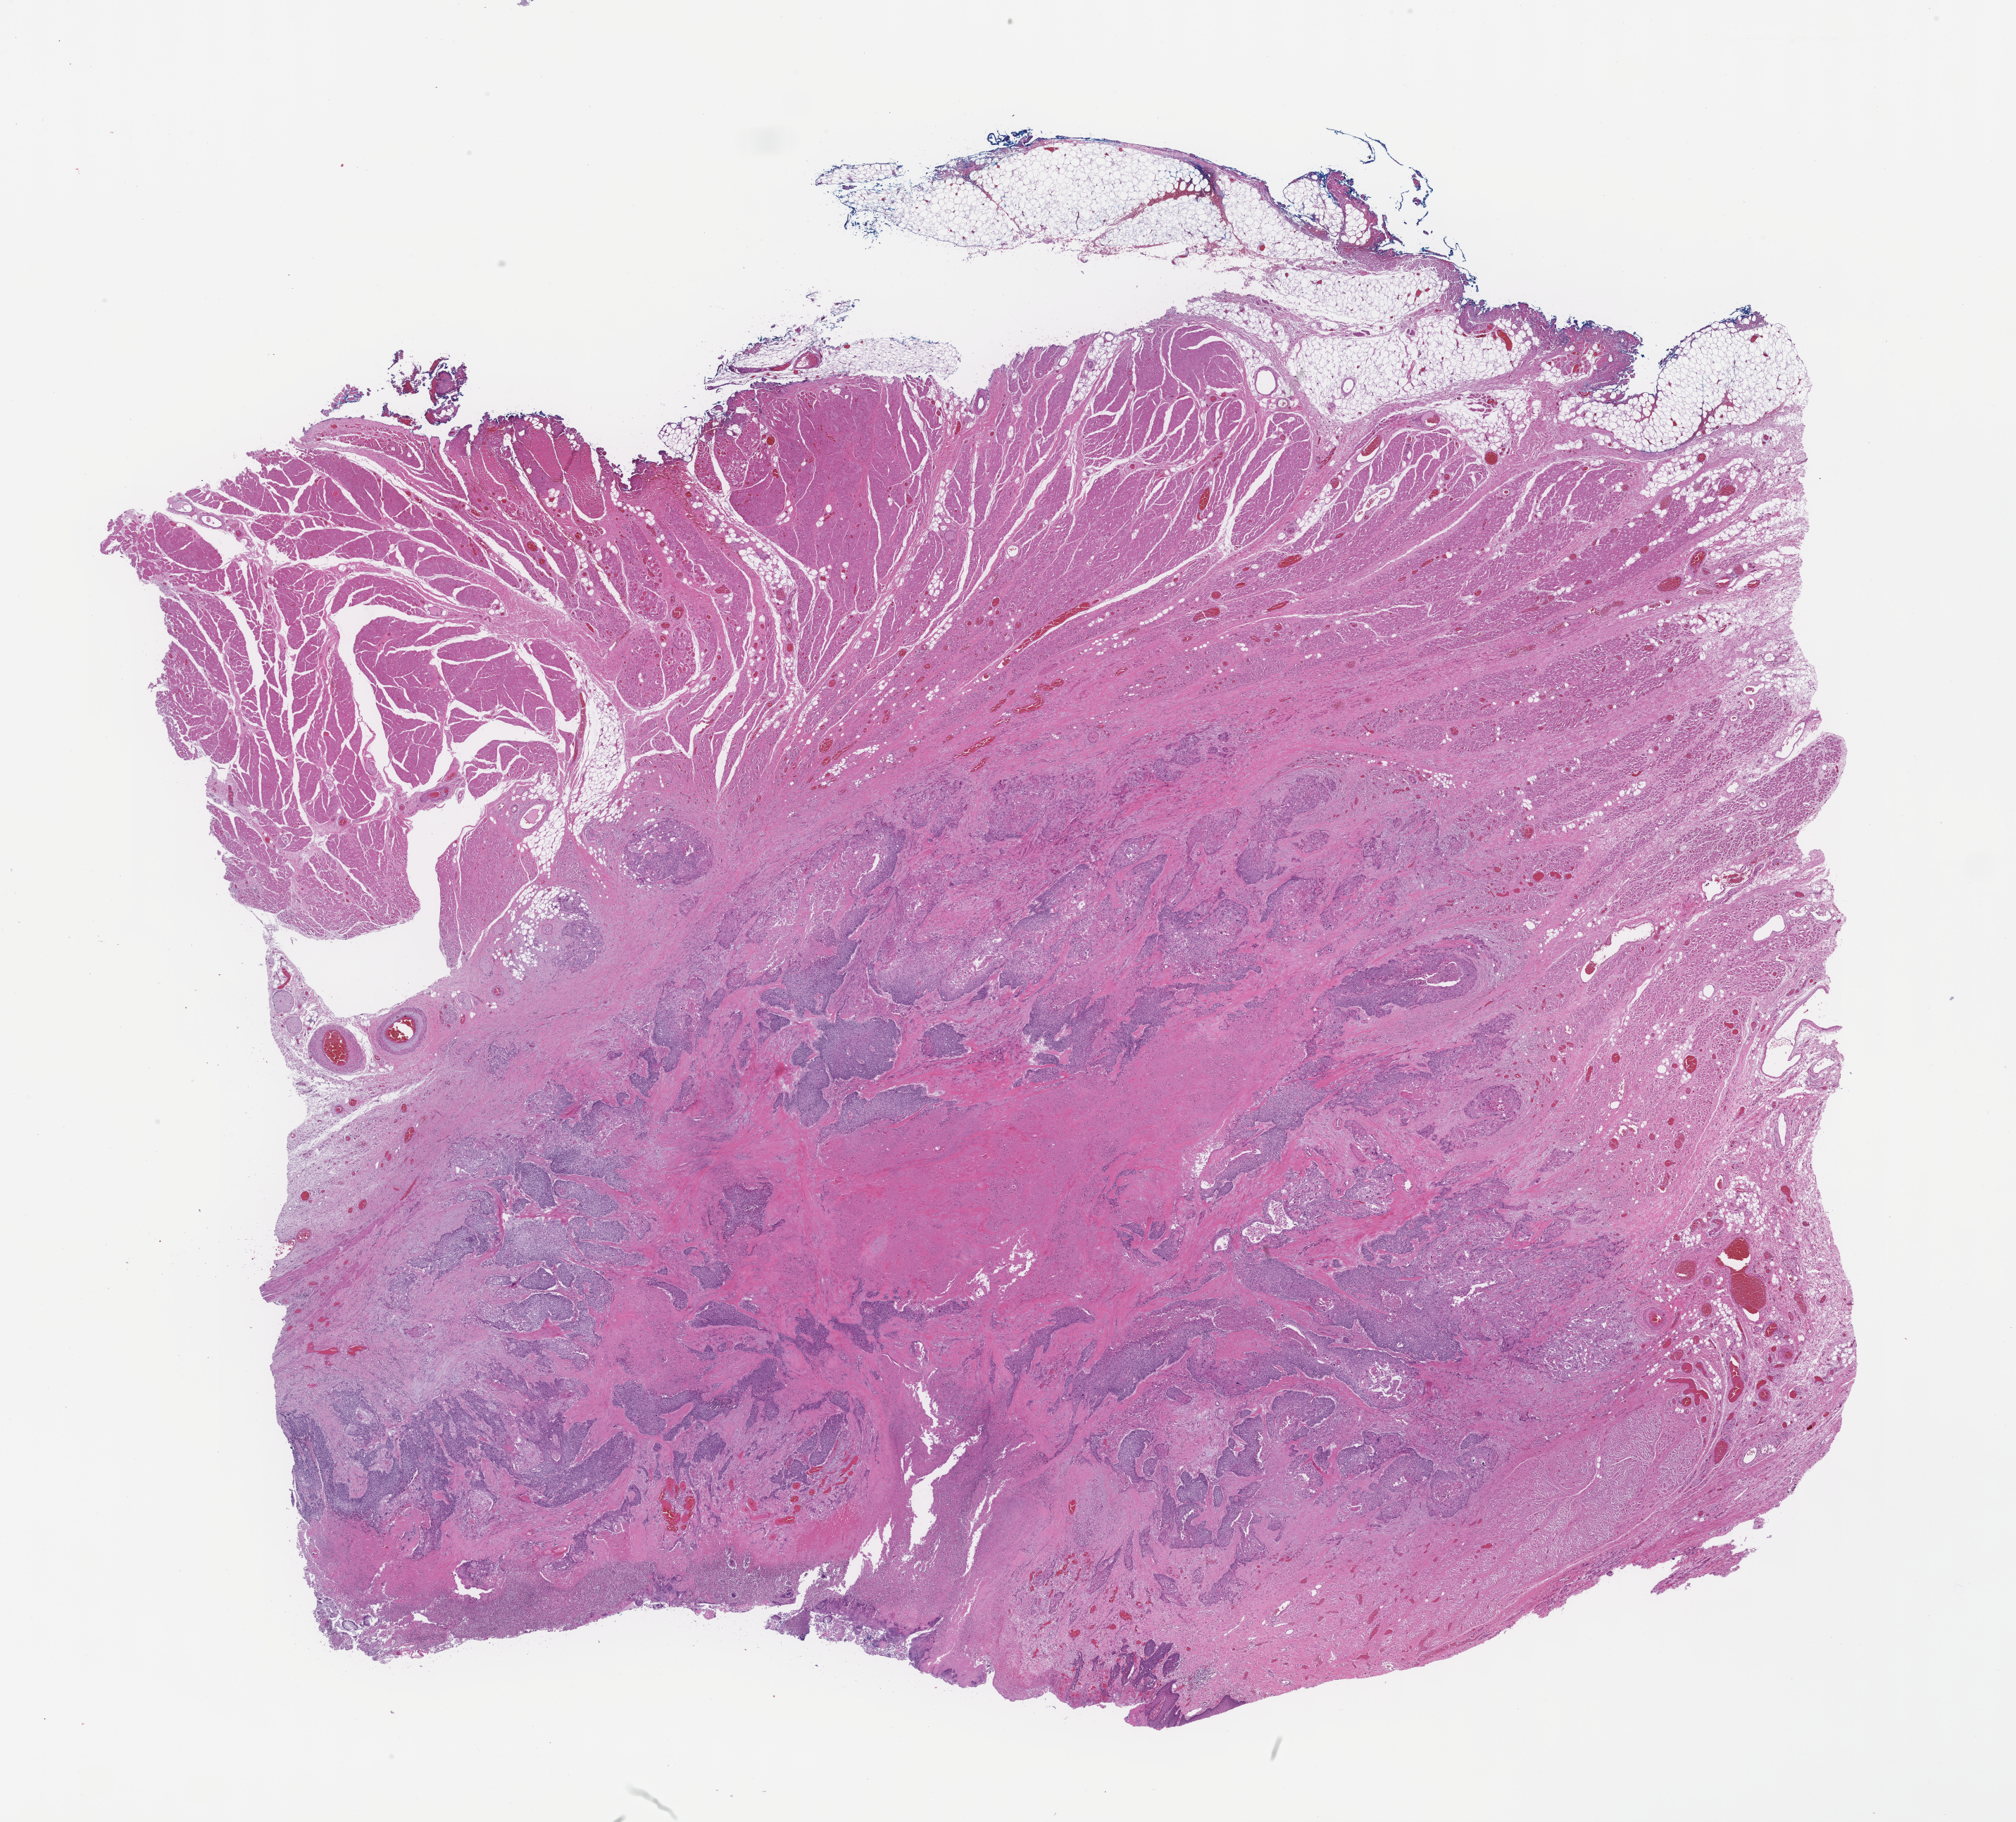
Digitized H&E-stained section, shown as a low-resolution overview of the whole scanned area (about 23.1 x 20.9 mm); FFPE section; tissue site: colon. Female patient.
This section: primary tumor. Diagnosis: Colorectal Carcinoma.